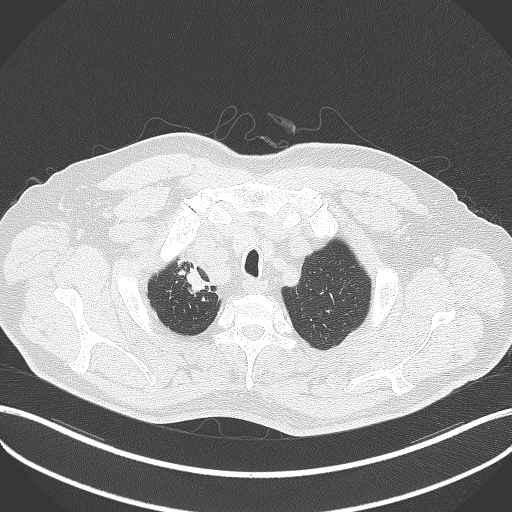
Chest CT, one axial slice. Position 344 of 411 along the scan axis. 120 kVp. Lung window (W 1500 / L -600 HU). 1 mm slice thickness. 512 × 512 image matrix. Patient: male, 60 years. From the clinical record (not read from this slice): clinical TNM (as recorded): T1b N1 M0.
Structures marked on this image (rectangle marked by the reading radiologist):
- lung tumour (recorded histology: squamous cell carcinoma): bounding box <182,258,211,296> (left, top, right, bottom; pixels)